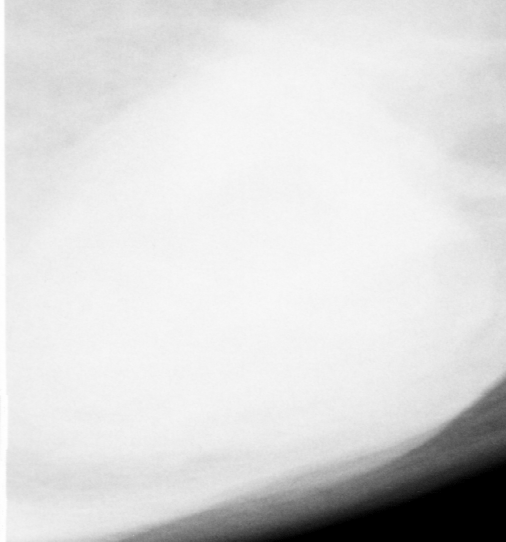
Cropped region of a digitized screen-film mammogram centred on a radiologist-marked abnormality, left breast, CC view.
Marked abnormality: mass, shape irregular, margins circumscribed / ill defined; BI-RADS assessment category 4; pathology (as recorded): malignant.